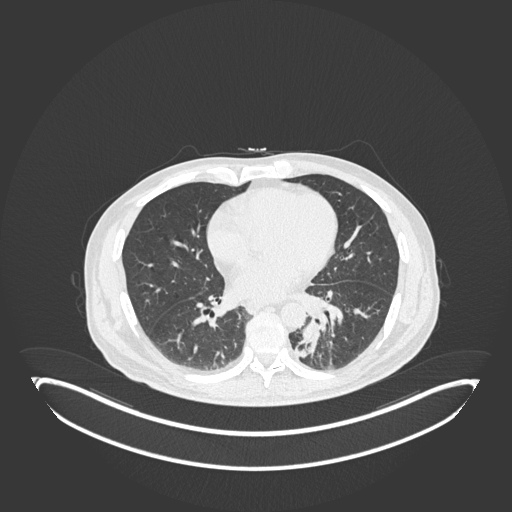
Chest CT, one axial slice. Slice 69 of 251 in the series (ordered by position). Reconstruction kernel B30f. Lung window (W 1500 / L -600 HU). 1 mm slice thickness. 512 × 512 image matrix, field of view 500 × 500 mm. Male patient, age 72 years. Case-level facts recorded for this patient, not image findings: clinical TNM (as recorded): T2b N0 M1.
Annotated regions visible in this slice (bounding box drawn by a radiologist):
- lung tumour (recorded histology: adenocarcinoma): box from (x=296, y=318) to (x=321, y=361) px